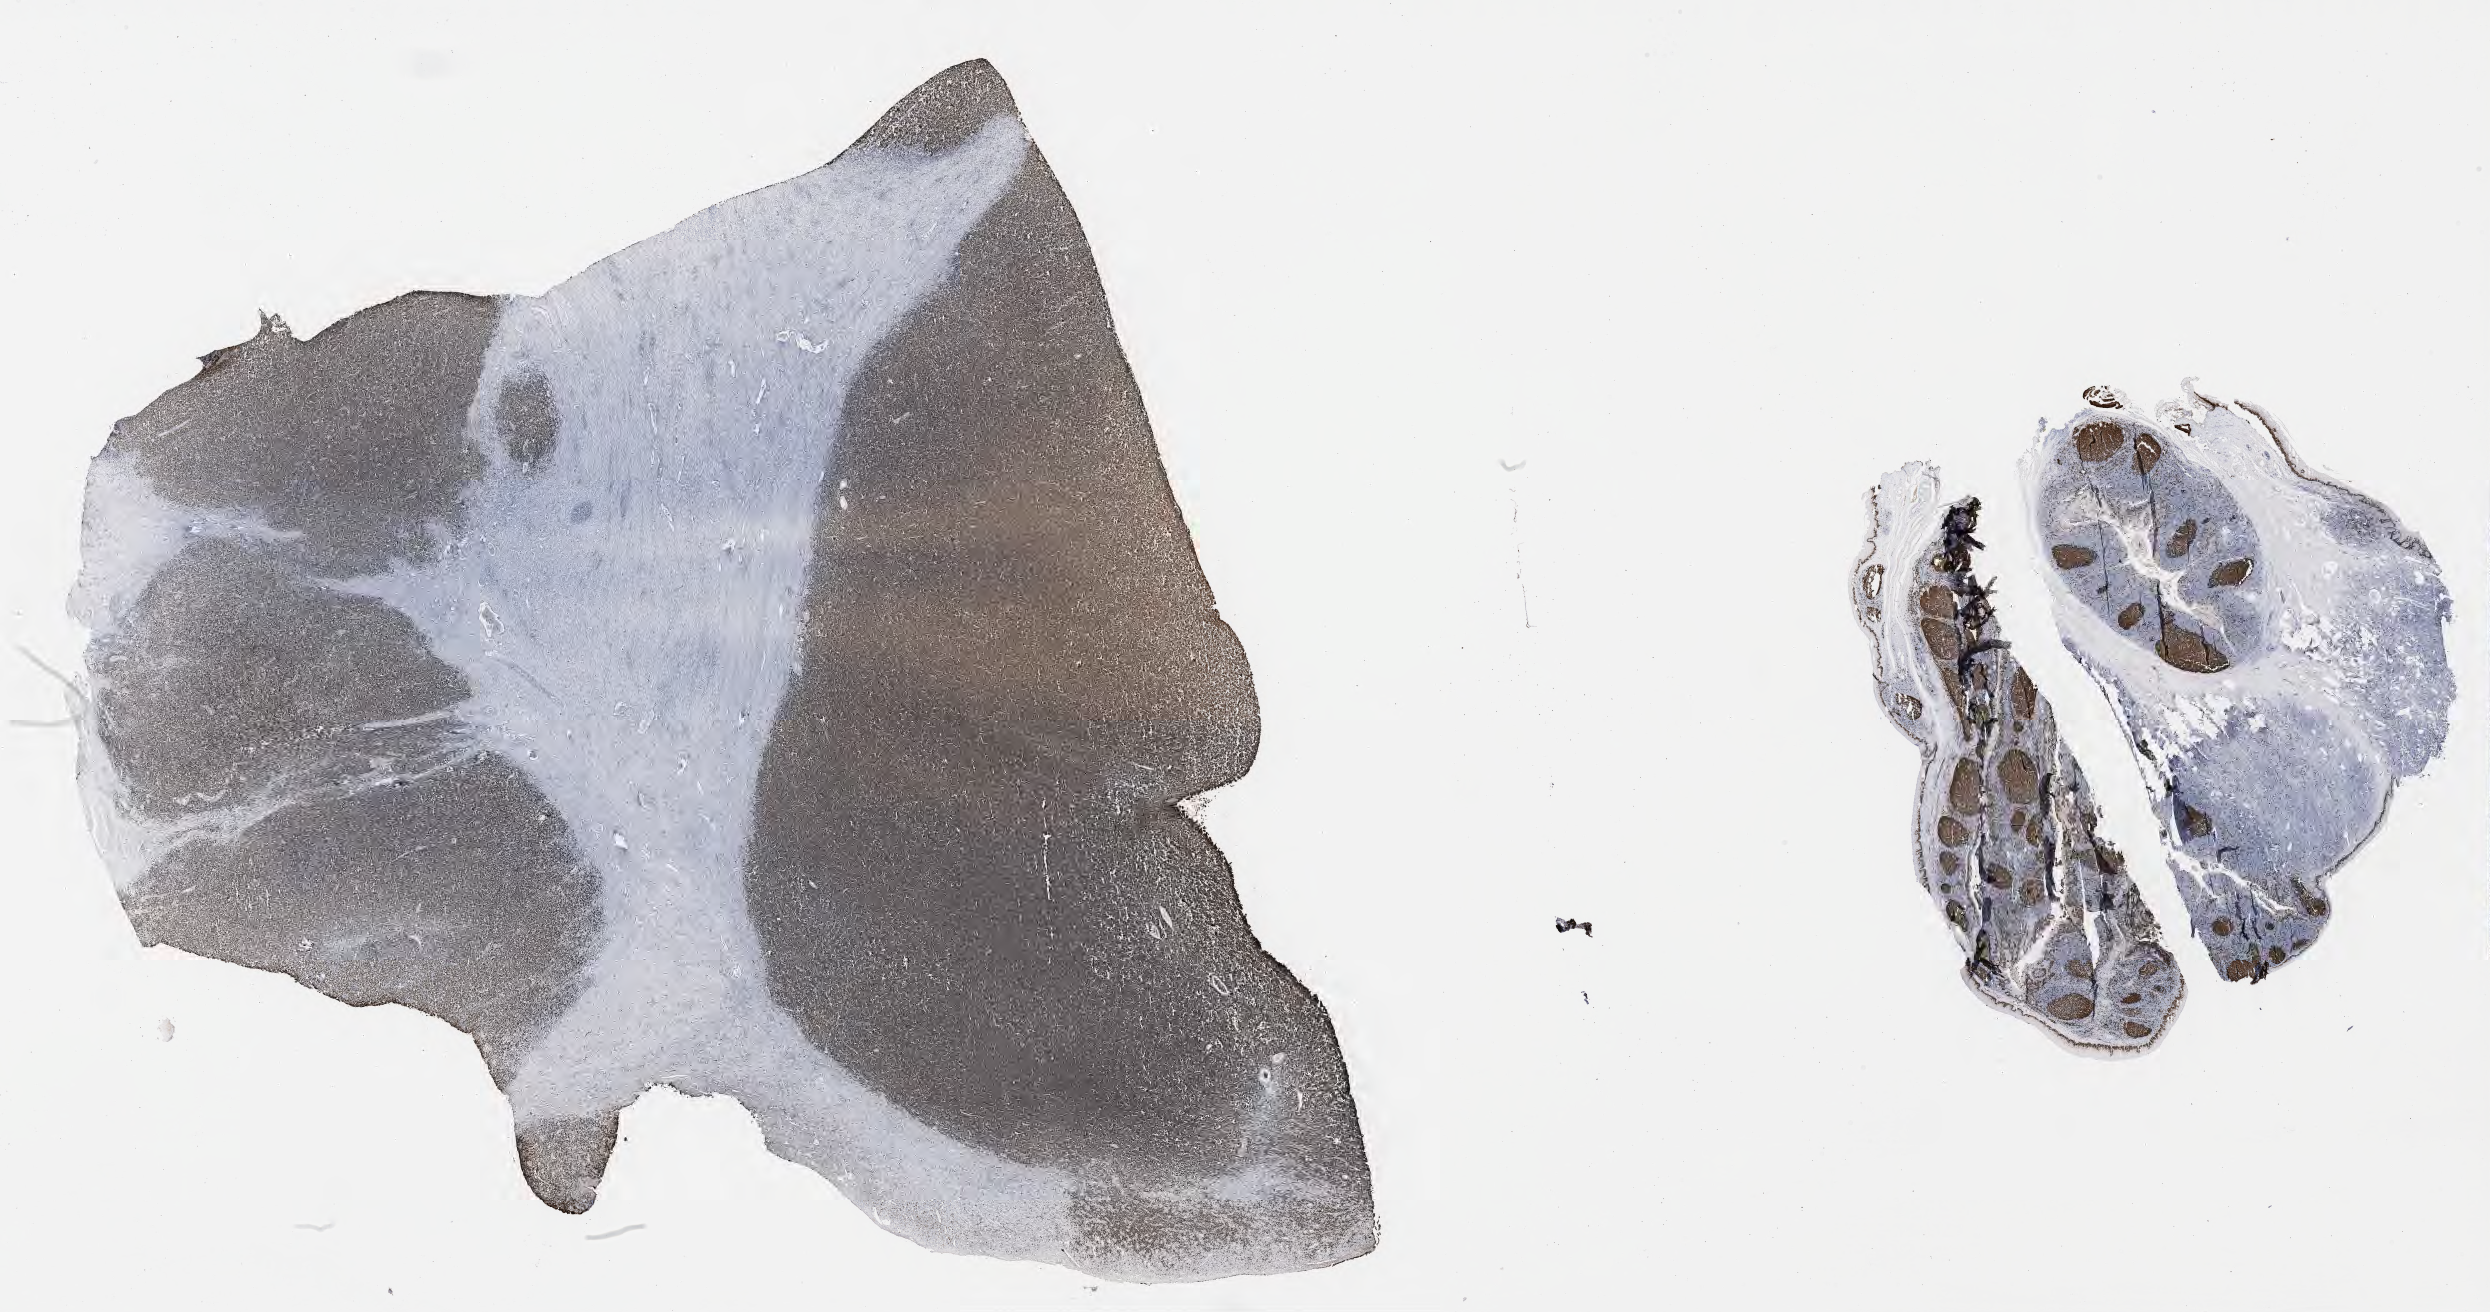
Whole-slide image, immunohistochemical stain for Ki-67 — whole scanned area (about 40.2 x 21.2 mm) shown as a low-resolution overview; tumor tissue. Female, age 8 years at initial diagnosis.
• histologic diagnosis: Burkitt lymphoma, NOS